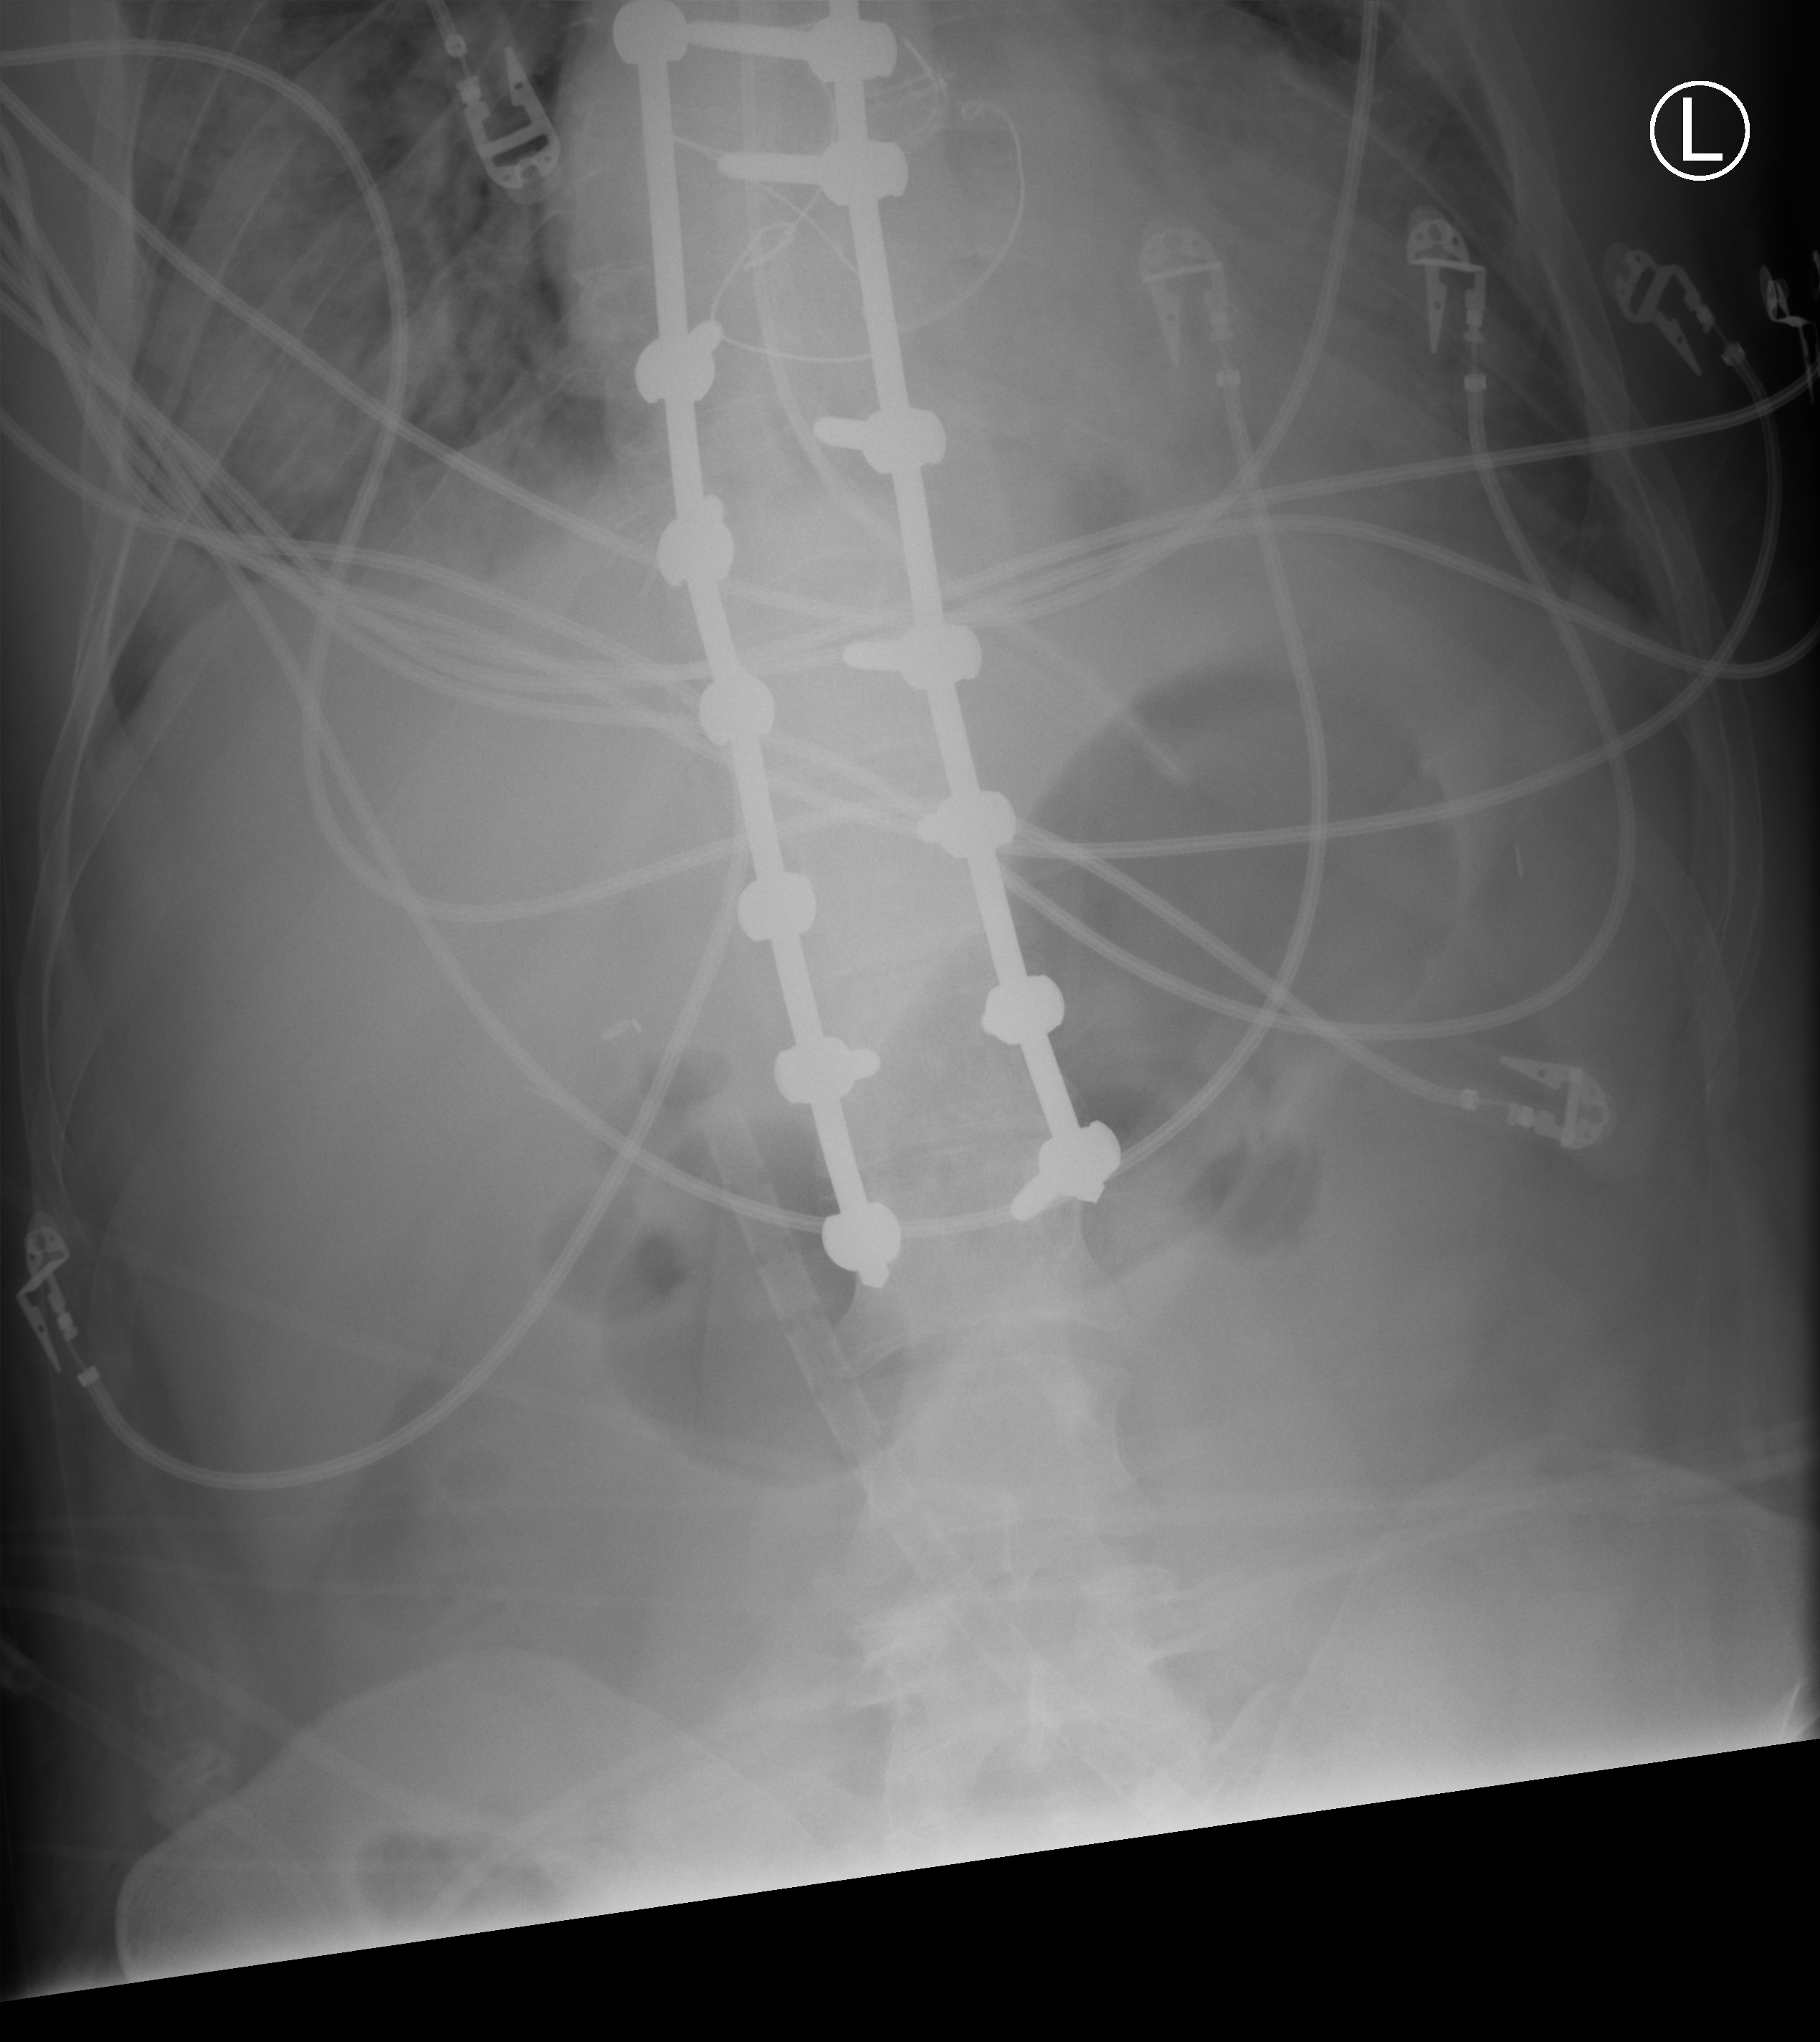
Abdomen X-ray; anteroposterior (AP) projection. Patient hospitalised with COVID-19, aged 18–59 years.
Hospital-stay facts (about this admission, not read from this image; timing relative to this image not recorded): admitted to intensive care during this hospital stay: yes; mechanically ventilated during this hospital stay: yes; diabetes (admission record): no.